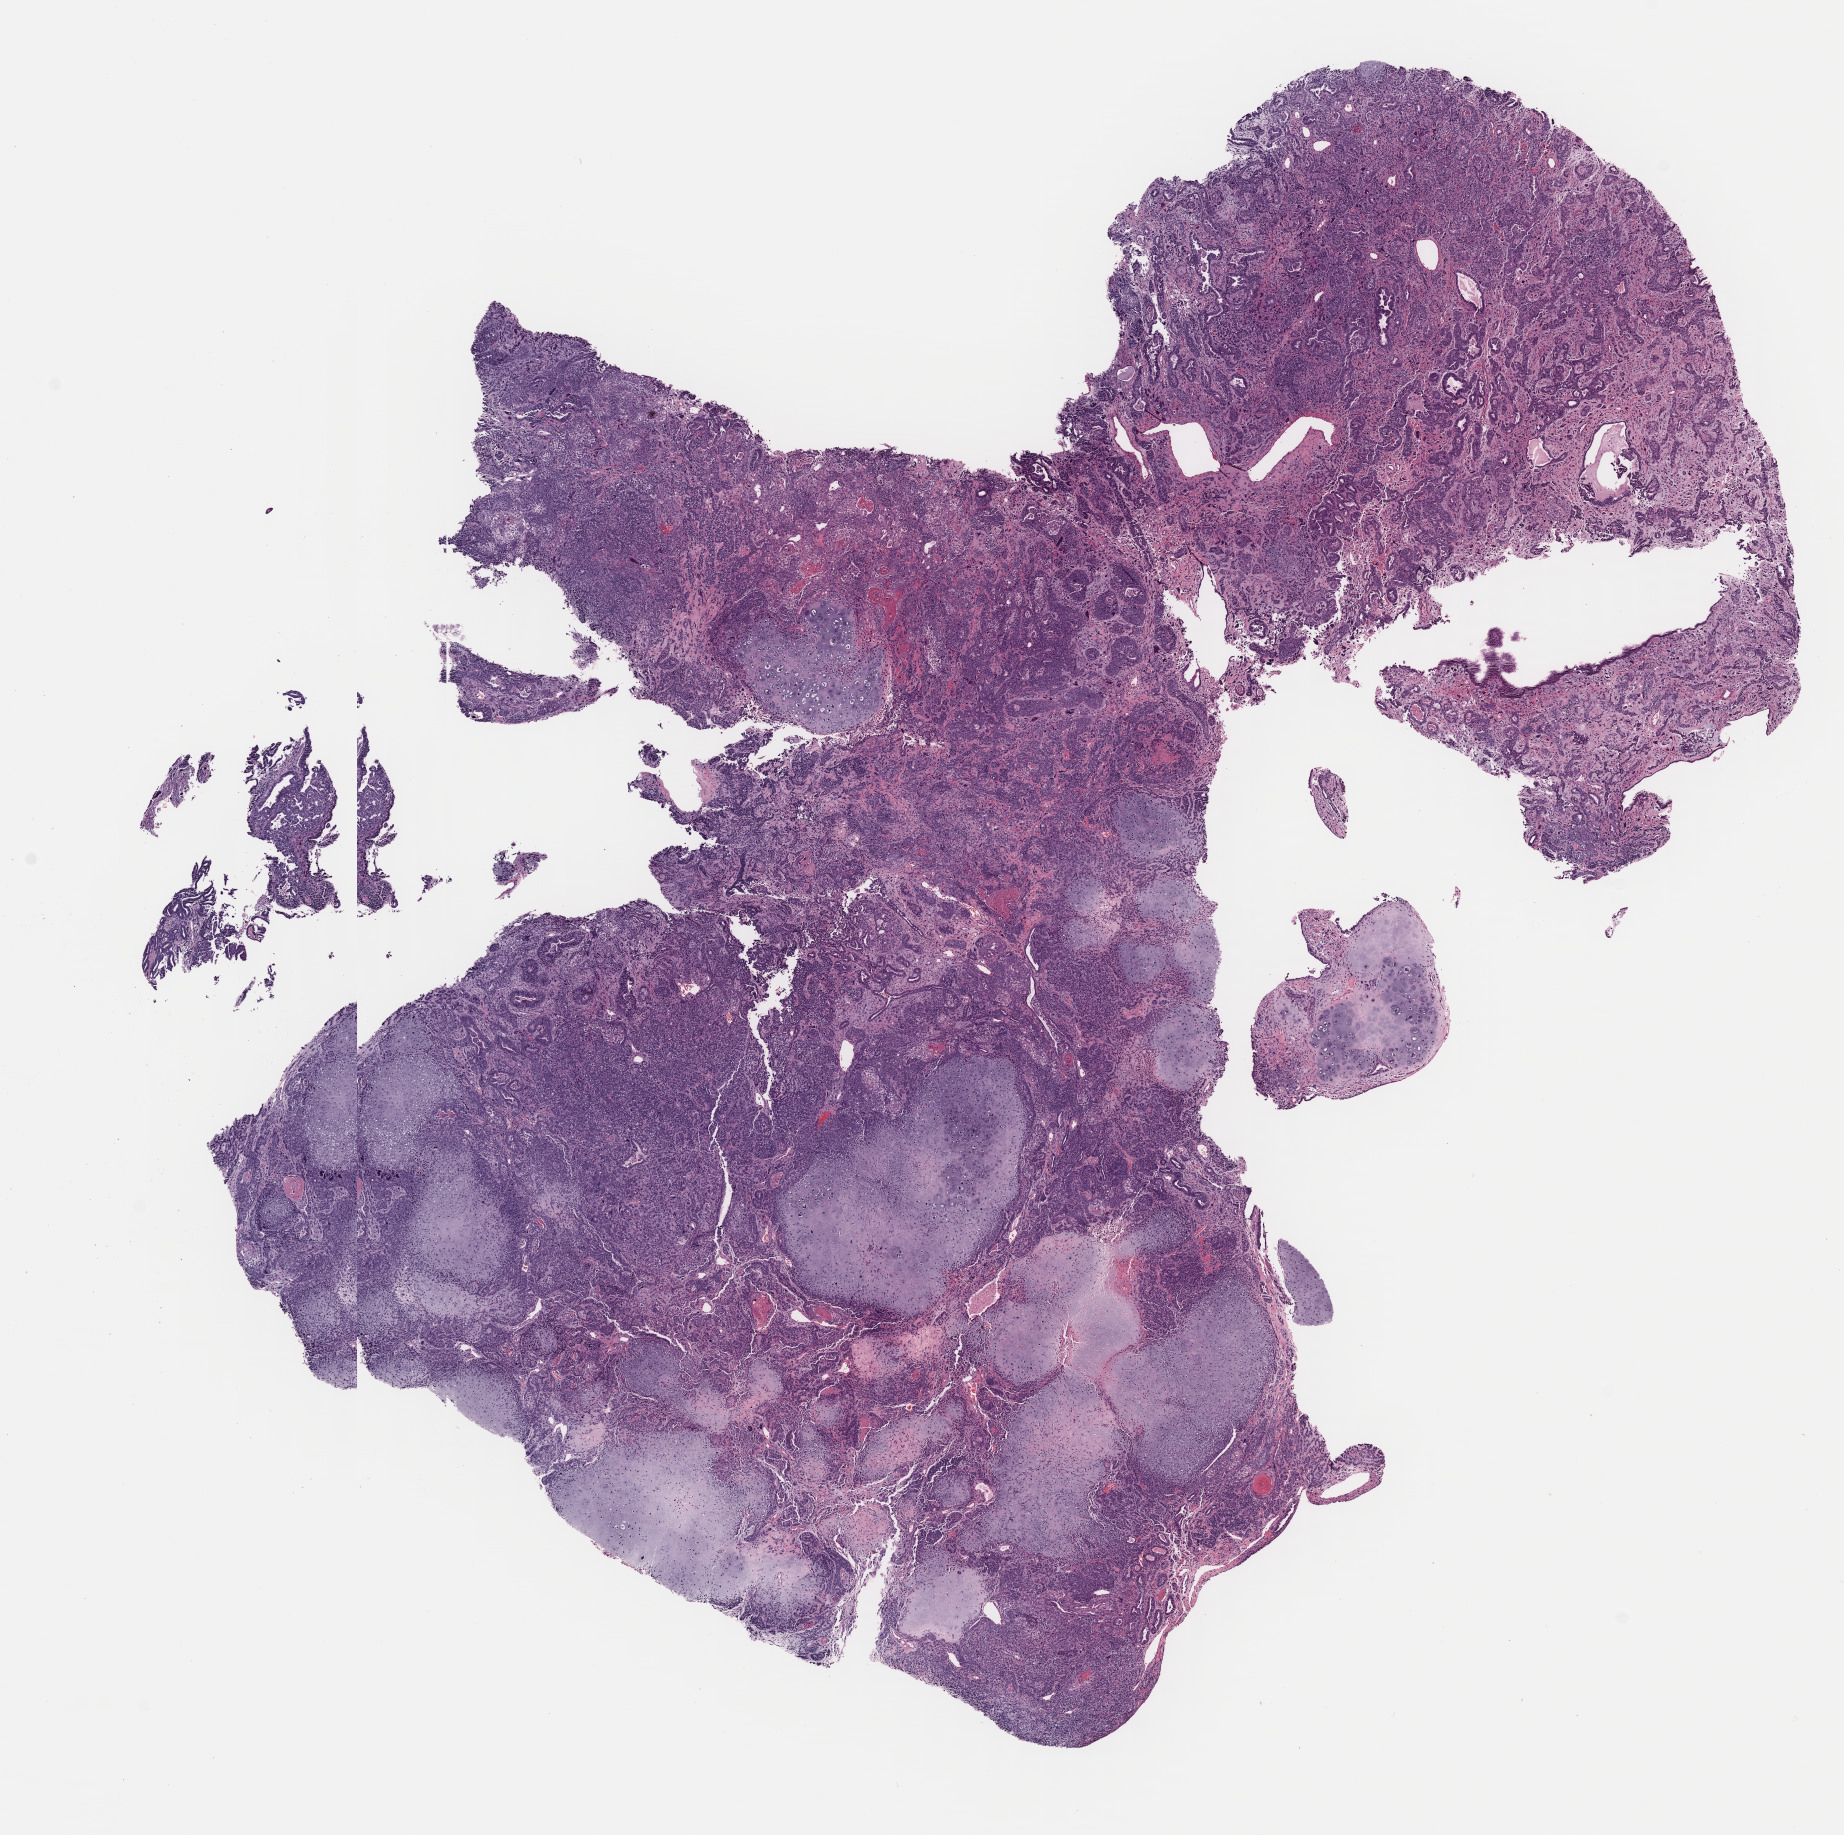
H&E-stained whole-slide image — shown as a low-resolution overview of the whole scanned area (about 14.5 x 14.5 mm, acquisition: 40x scan); FFPE section; uterus, primary tumour sample. Patient: female, age at initial diagnosis 84 years.
Histologic diagnosis: Mullerian mixed tumor (endometrium). FIGO stage: IIIC.